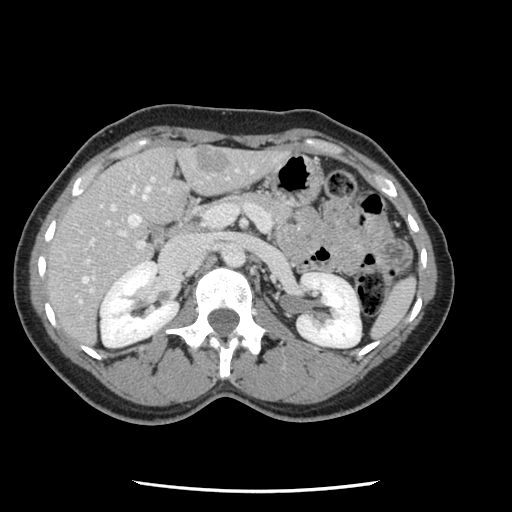
Contrast-enhanced abdominal CT, one axial slice. Slice 59 of 134 in the series (ordered by position). 120 kVp. Intravenous contrast given. Soft-tissue window (W 400 / L 40 HU). 2.5 mm slice thickness. 512 × 512 image matrix, field of view 330 × 330 mm. Female patient, age 43 years. Case-level facts recorded for this patient, not image findings: diagnosis: colorectal cancer liver metastases, imaged before liver resection; multiple liver metastases: yes; largest metastasis: 3.4 cm; chemotherapy before resection: no.
Annotated regions visible in this slice (outlined manually by an expert reader):
- hepatic veins: bounding box (x1, y1, x2, y2) in pixels: (82, 178, 154, 283)
- liver: (46, 146, 287, 347)
- planned liver remnant (the part of the liver to remain after resection): (46, 147, 184, 319)
- portal vein (with intrahepatic branches): (84, 170, 272, 294)
- liver metastasis: (195, 151, 229, 173)